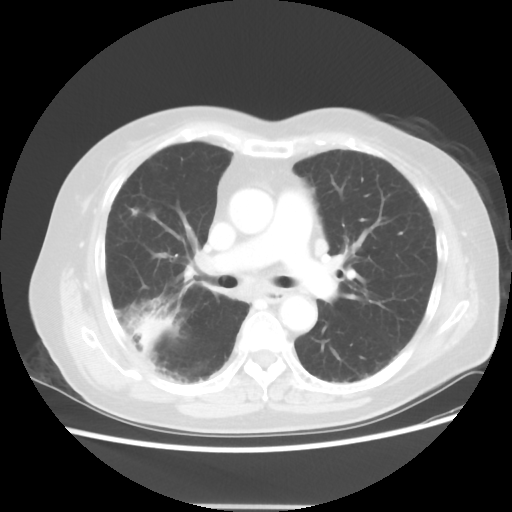
Chest CT, one axial slice; position 28 of 50 along the scan axis; reconstruction kernel STANDARD; lung window (W 1500 / L -600 HU); 512 × 512 image matrix, field of view 360 × 360 mm. Patient: female, 72 years. Case-level facts recorded for this patient, not image findings: clinical TNM (as recorded): T2 N1 M0.
Structures marked on this image (rectangle marked by the reading radiologist):
- lung tumour (recorded histology: adenocarcinoma): bounding box (x1, y1, x2, y2) in pixels: (130, 311, 173, 356)